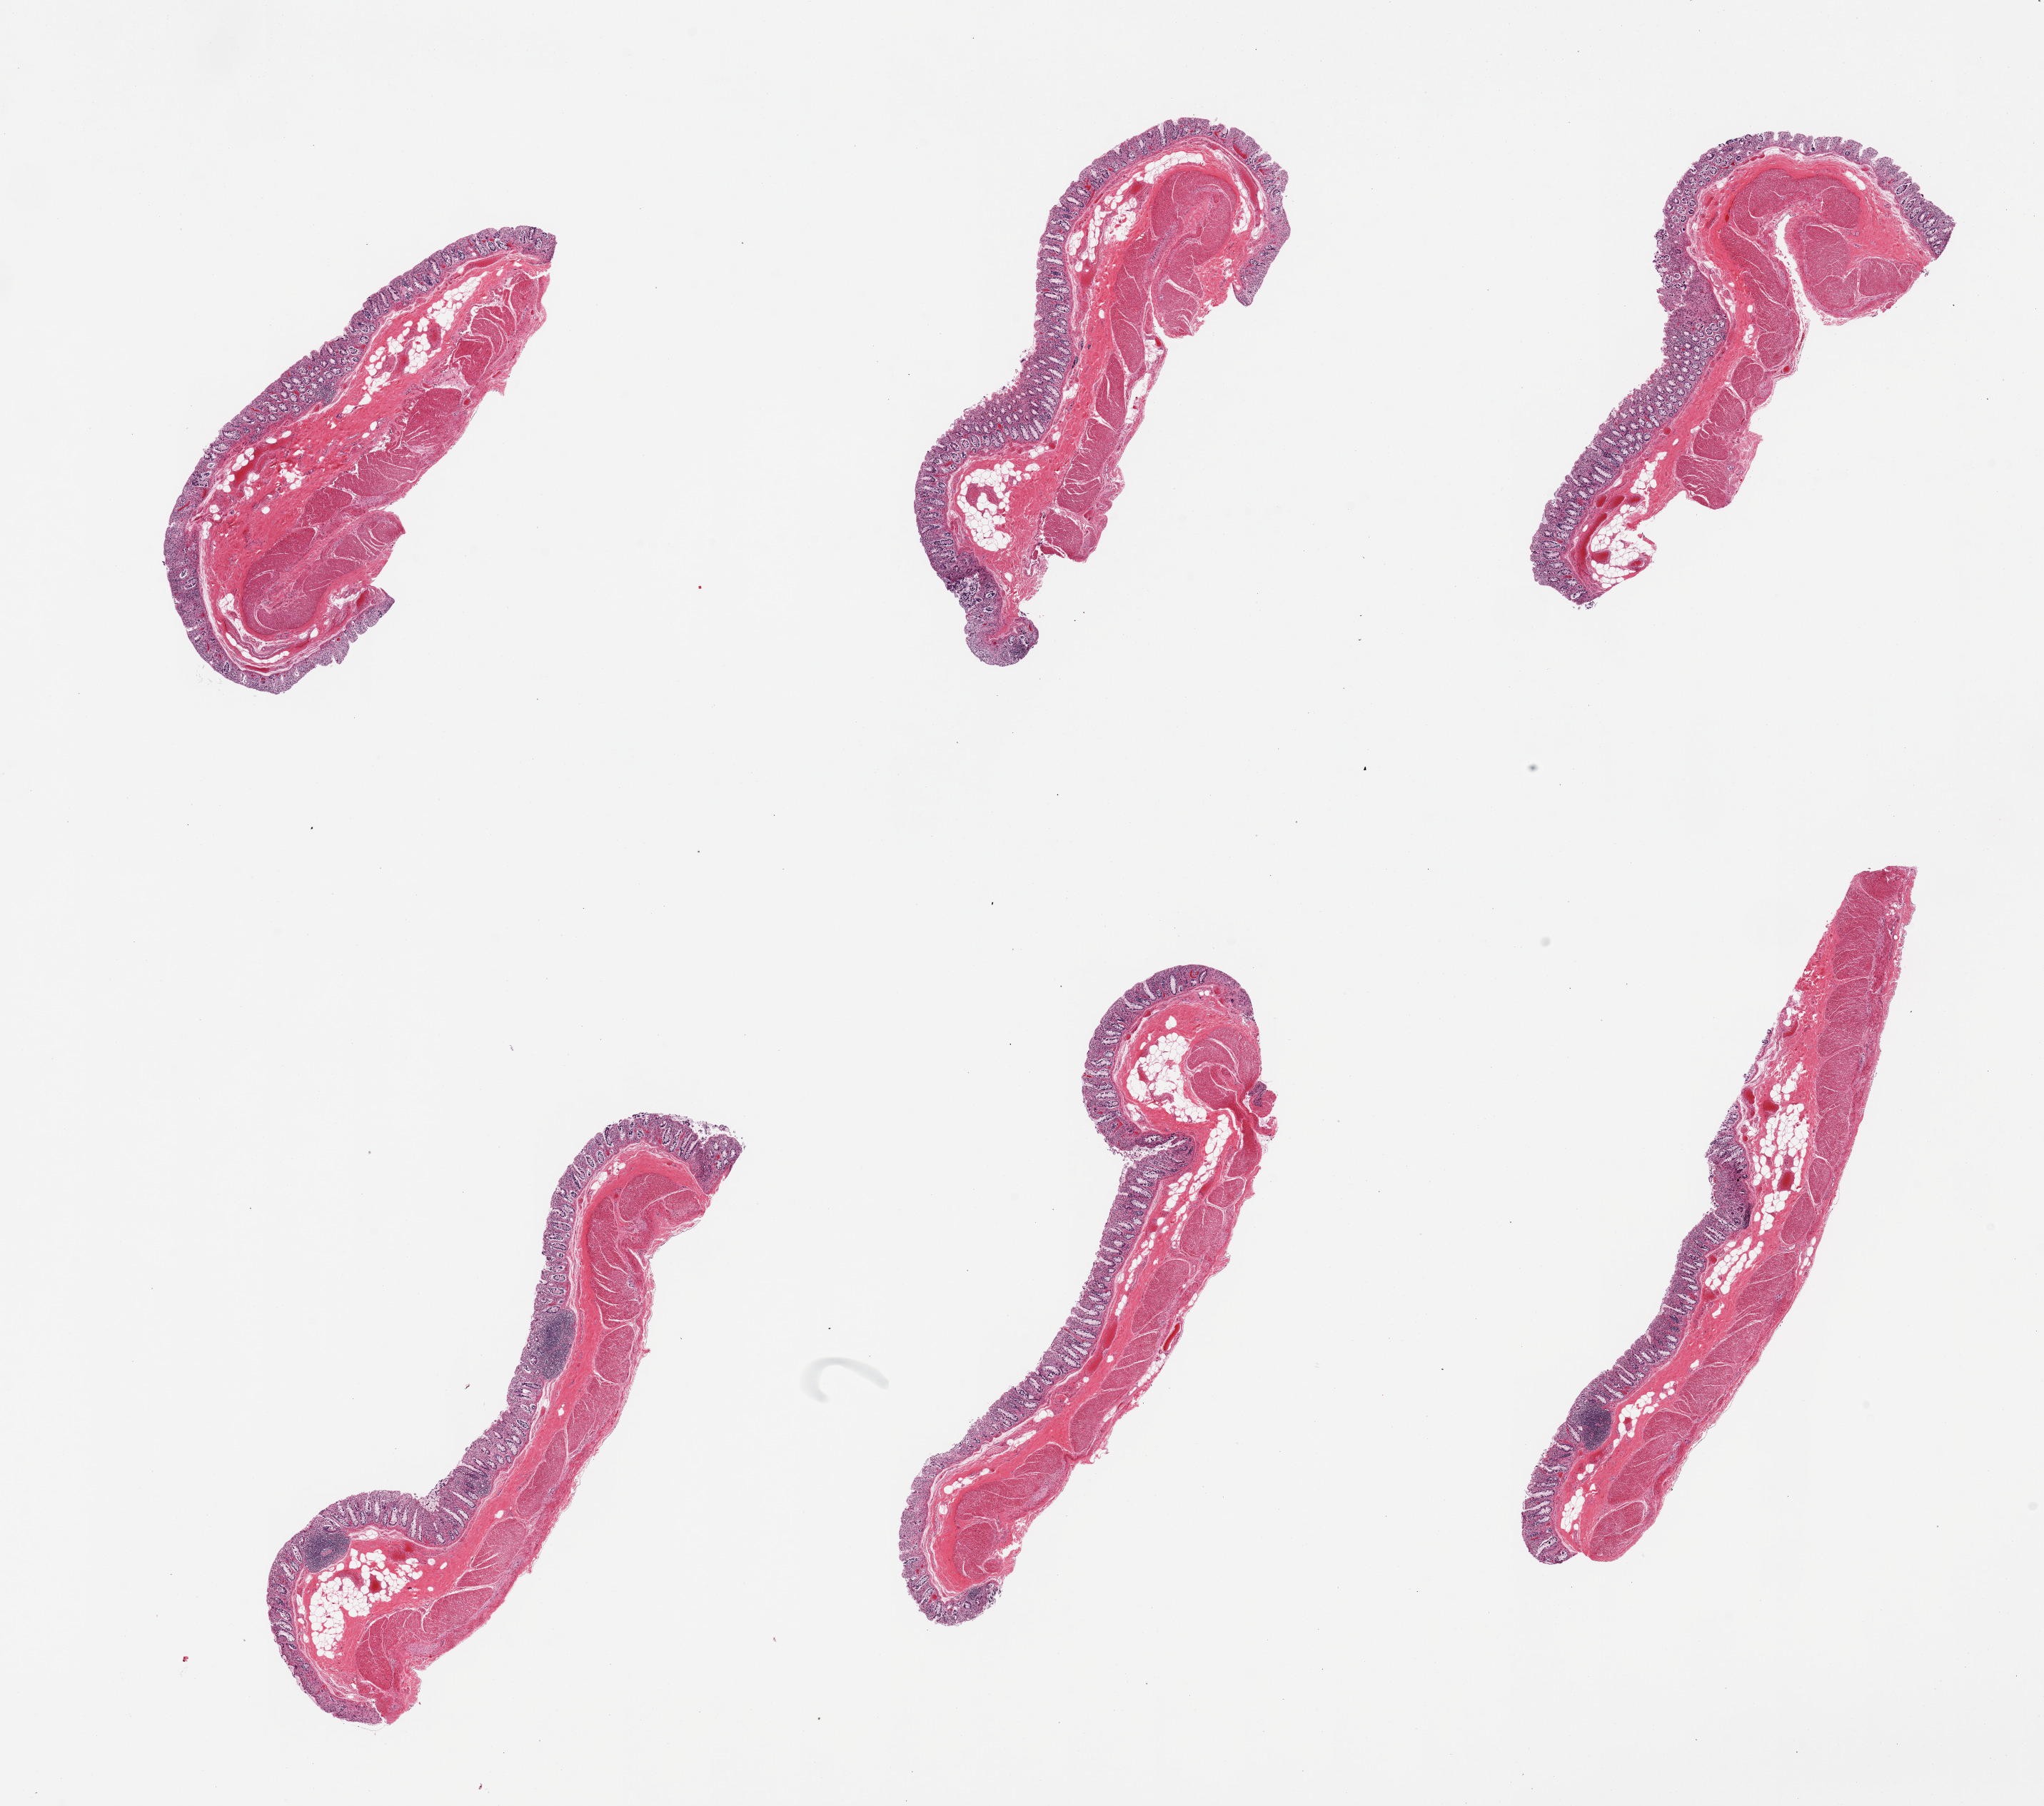
Whole-slide image, hematoxylin and eosin (H&E) stain — shown as a low-resolution overview of the whole scanned area (about 22.6 x 20.0 mm, slide scanned at 20x); PAXgene-fixed paraffin-embedded (PFPE) section; sampled site (target tissue): transverse colon; donor tissue sample. Donor sex: male.
Reviewer comment on this tissue sample: 6 pieces. well dissected full thickness.